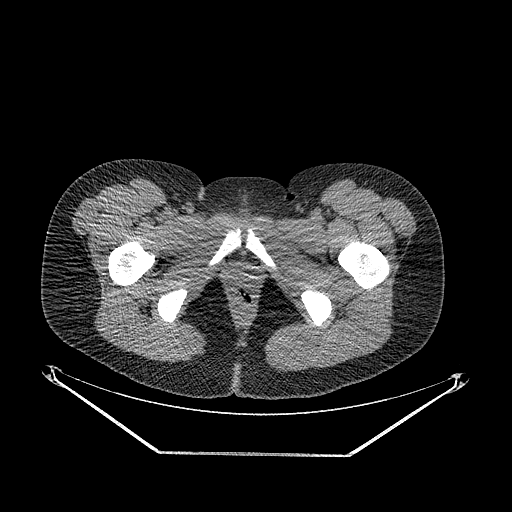
CT of an extremity soft-tissue mass (from a PET/CT study), one axial slice; reconstruction kernel STANDARD; 120 kVp; soft-tissue window (W 400 / L 40 HU); 3.75 mm slice thickness; 512 × 512 image matrix, field of view 500 × 500 mm. Female patient. From the clinical record (not read from this slice): histological type: epithelioid sarcoma; grade: intermediate; site of the primary tumour: right buttock.
Annotated regions visible in this slice (expert contour drawn on MRI and transferred to this co-registered scan by the dataset authors):
- gross tumour volume including surrounding oedema: box from (x=192, y=301) to (x=211, y=321) px